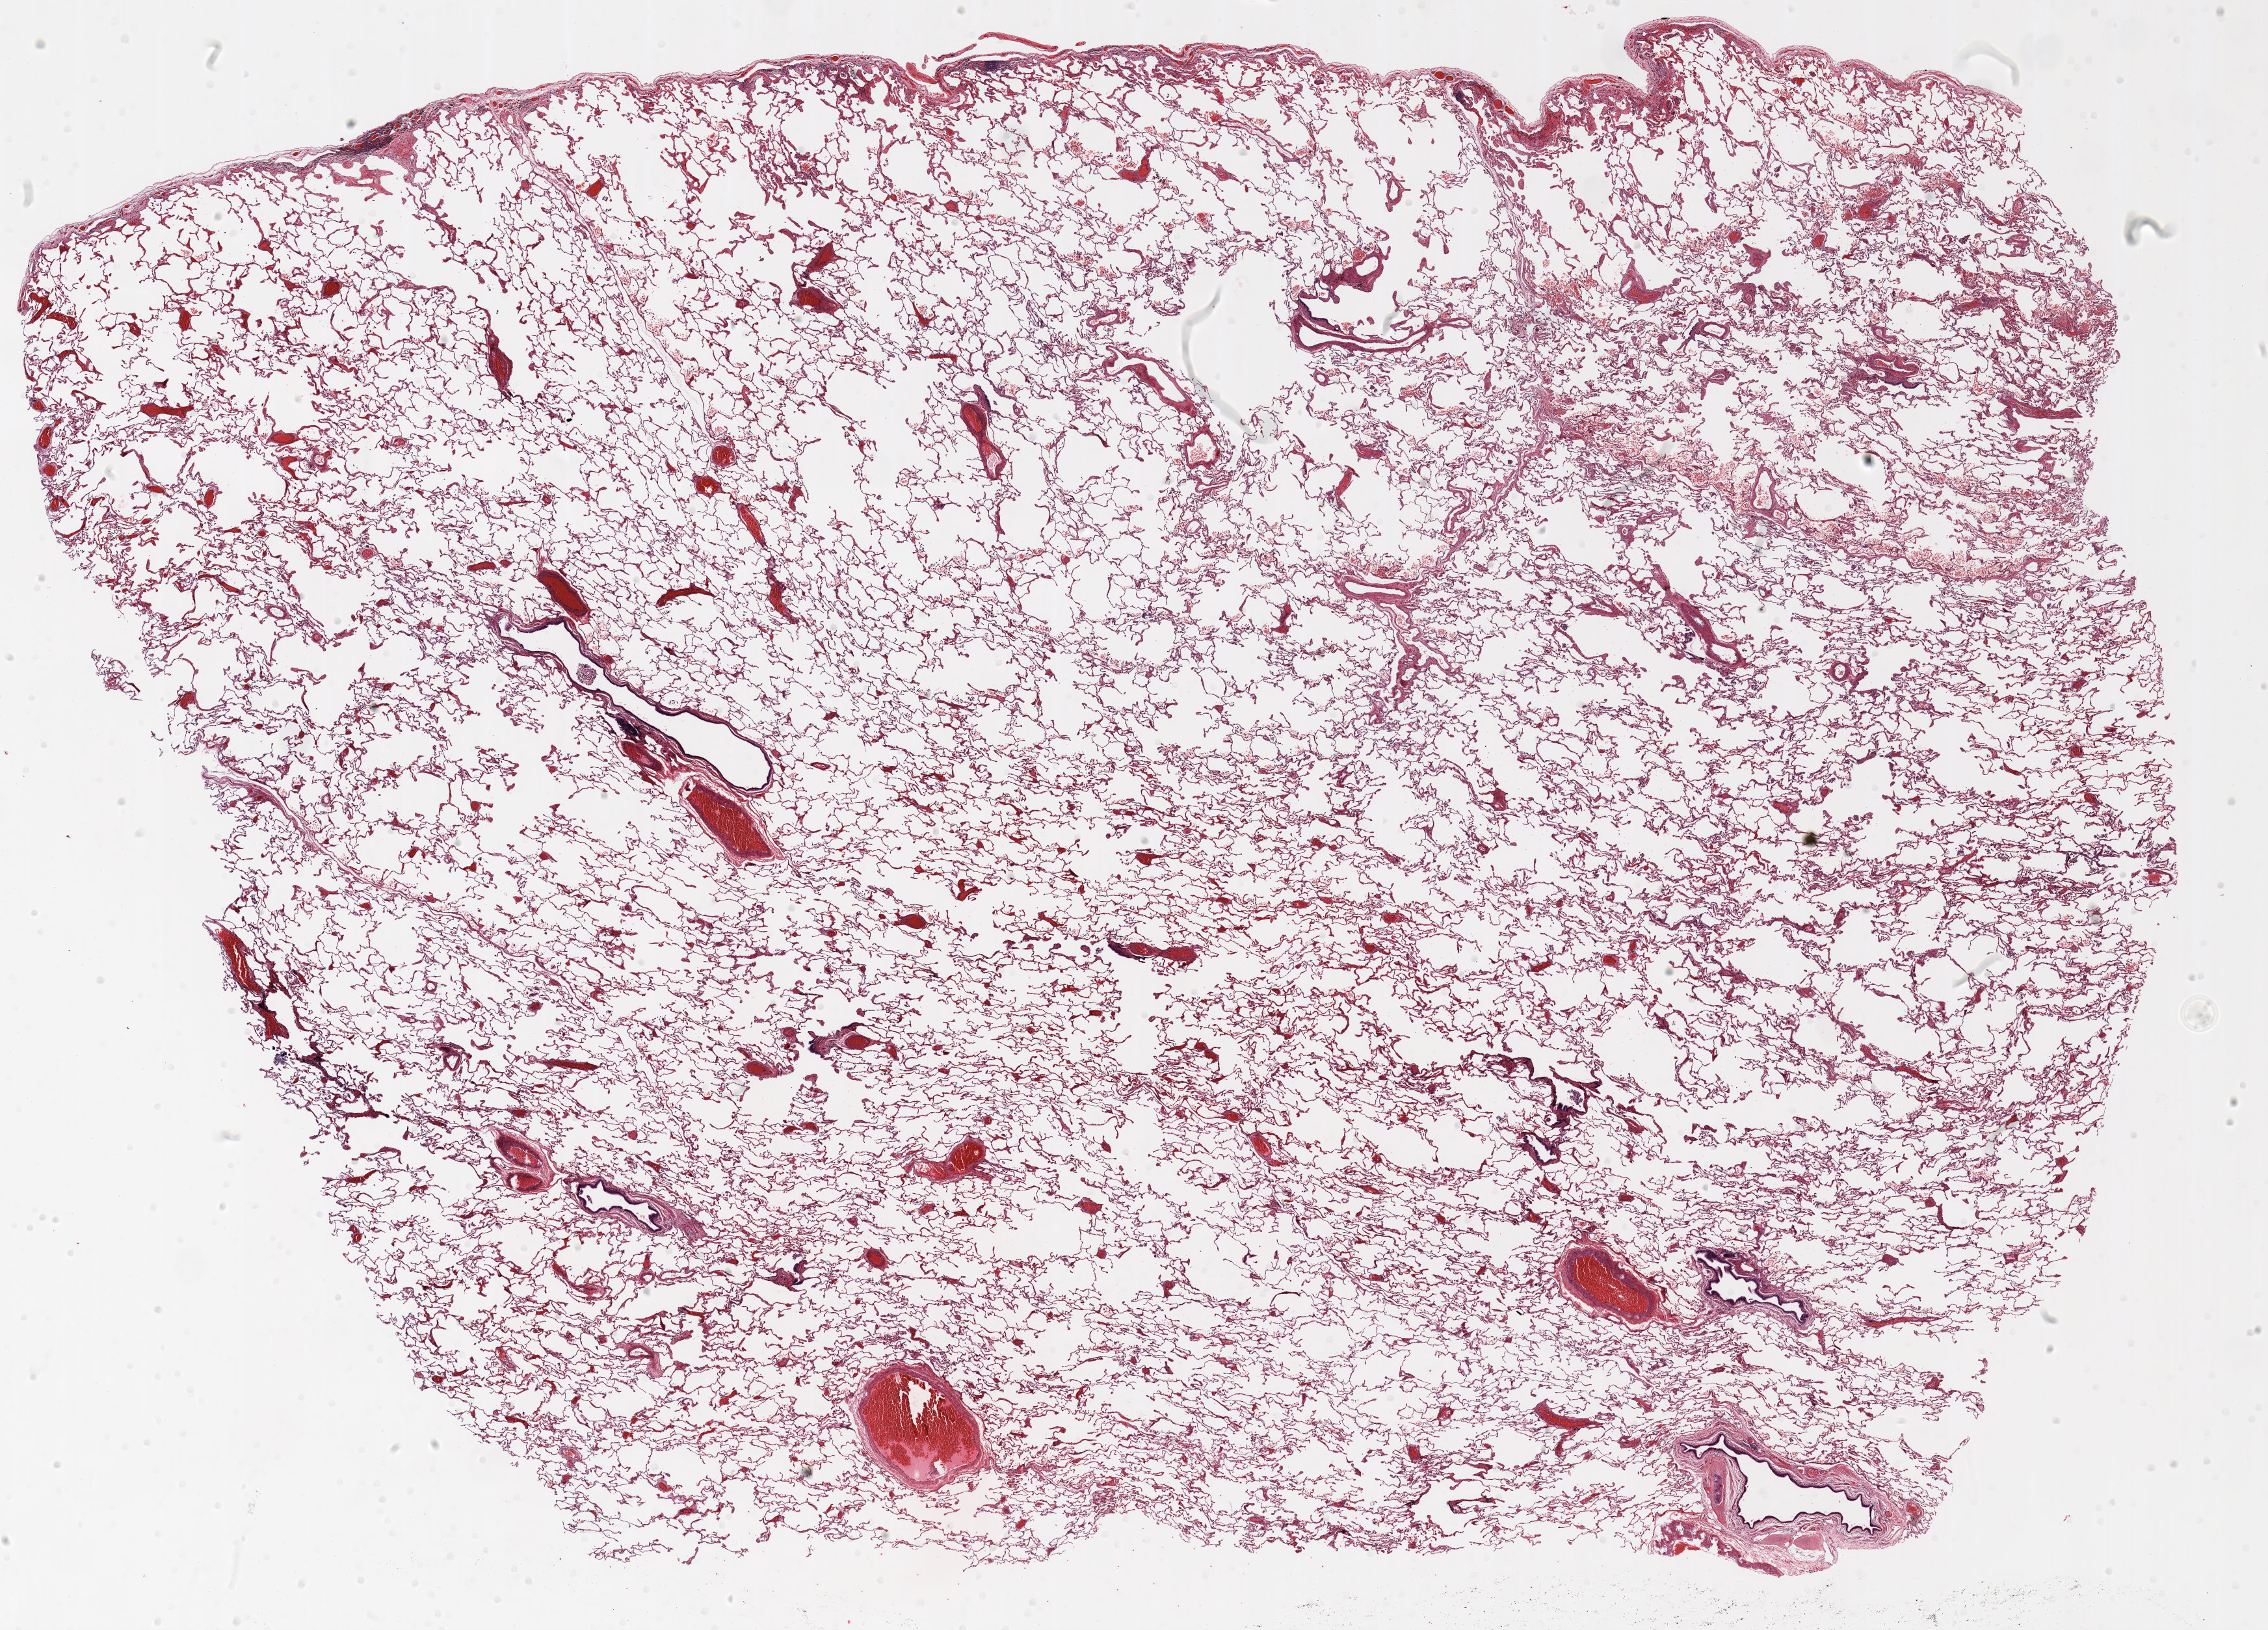
Whole-slide histology image, H&E-stained, whole scanned area (about 28.0 x 20.1 mm, slide scanned at 20x) shown as a low-resolution overview, FFPE section, lung tissue. Male, age 69 at enrolment. Grade: poorly differentiated (G3).
Primary tumour location (clinical record): right upper lobe. Stage (AJCC 6th edition): IB. ICD-O-3 topography: upper lobe of lung (C34.1). Participant's lung-cancer diagnosis: Adenocarcinoma, NOS. Tumour size (pathology): 40 mm.